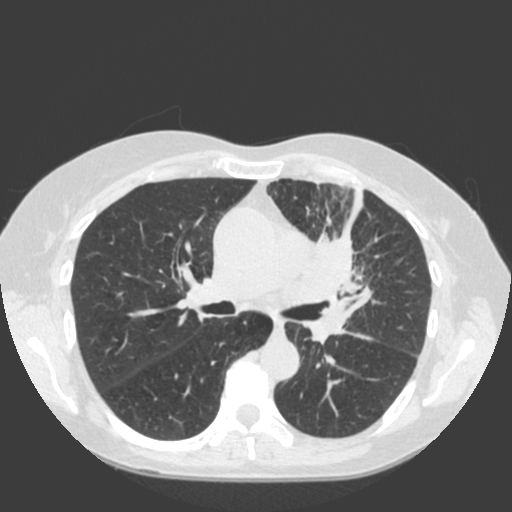
Low-dose screening chest CT, one axial slice. Slice 115 of 184 in the series (ordered by position). 120 kVp. Lung window (W 1500 / L -600 HU). 2 mm slice thickness. 512 × 512 image matrix.
Outlined on this slice (outlined manually by an expert reader):
- lesion 1 (tumor, hilum of left lung): box from (x=299, y=231) to (x=374, y=346) px